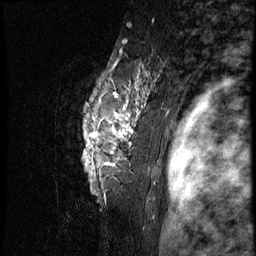
Breast MRI (dynamic contrast-enhanced), one sagittal slice; slice 59 of 66 in the series (ordered by position); 3 images stored at this slice position (order not interpretable as contrast timing); 1.5 T; TE 4.2 ms, TR 8.9 ms; 2.5 mm slice thickness; 256 × 256 image matrix, field of view 200 × 200 mm. Female patient, age 39 years. From the clinical record (not read from this slice): setting: breast cancer imaged before/during neoadjuvant chemotherapy; receptor status: HER2-positive.
Structures marked on this image (semi-automatically segmented with operator editing):
- analysis volume of interest (the breast-tissue region the enhancement analysis was run in; not a lesion): box from (x=56, y=44) to (x=166, y=196) px
- tumour enhancement mask (voxels above the 140 % enhancement threshold inside the analysis volume of interest): (x=90, y=89)–(x=145, y=164)